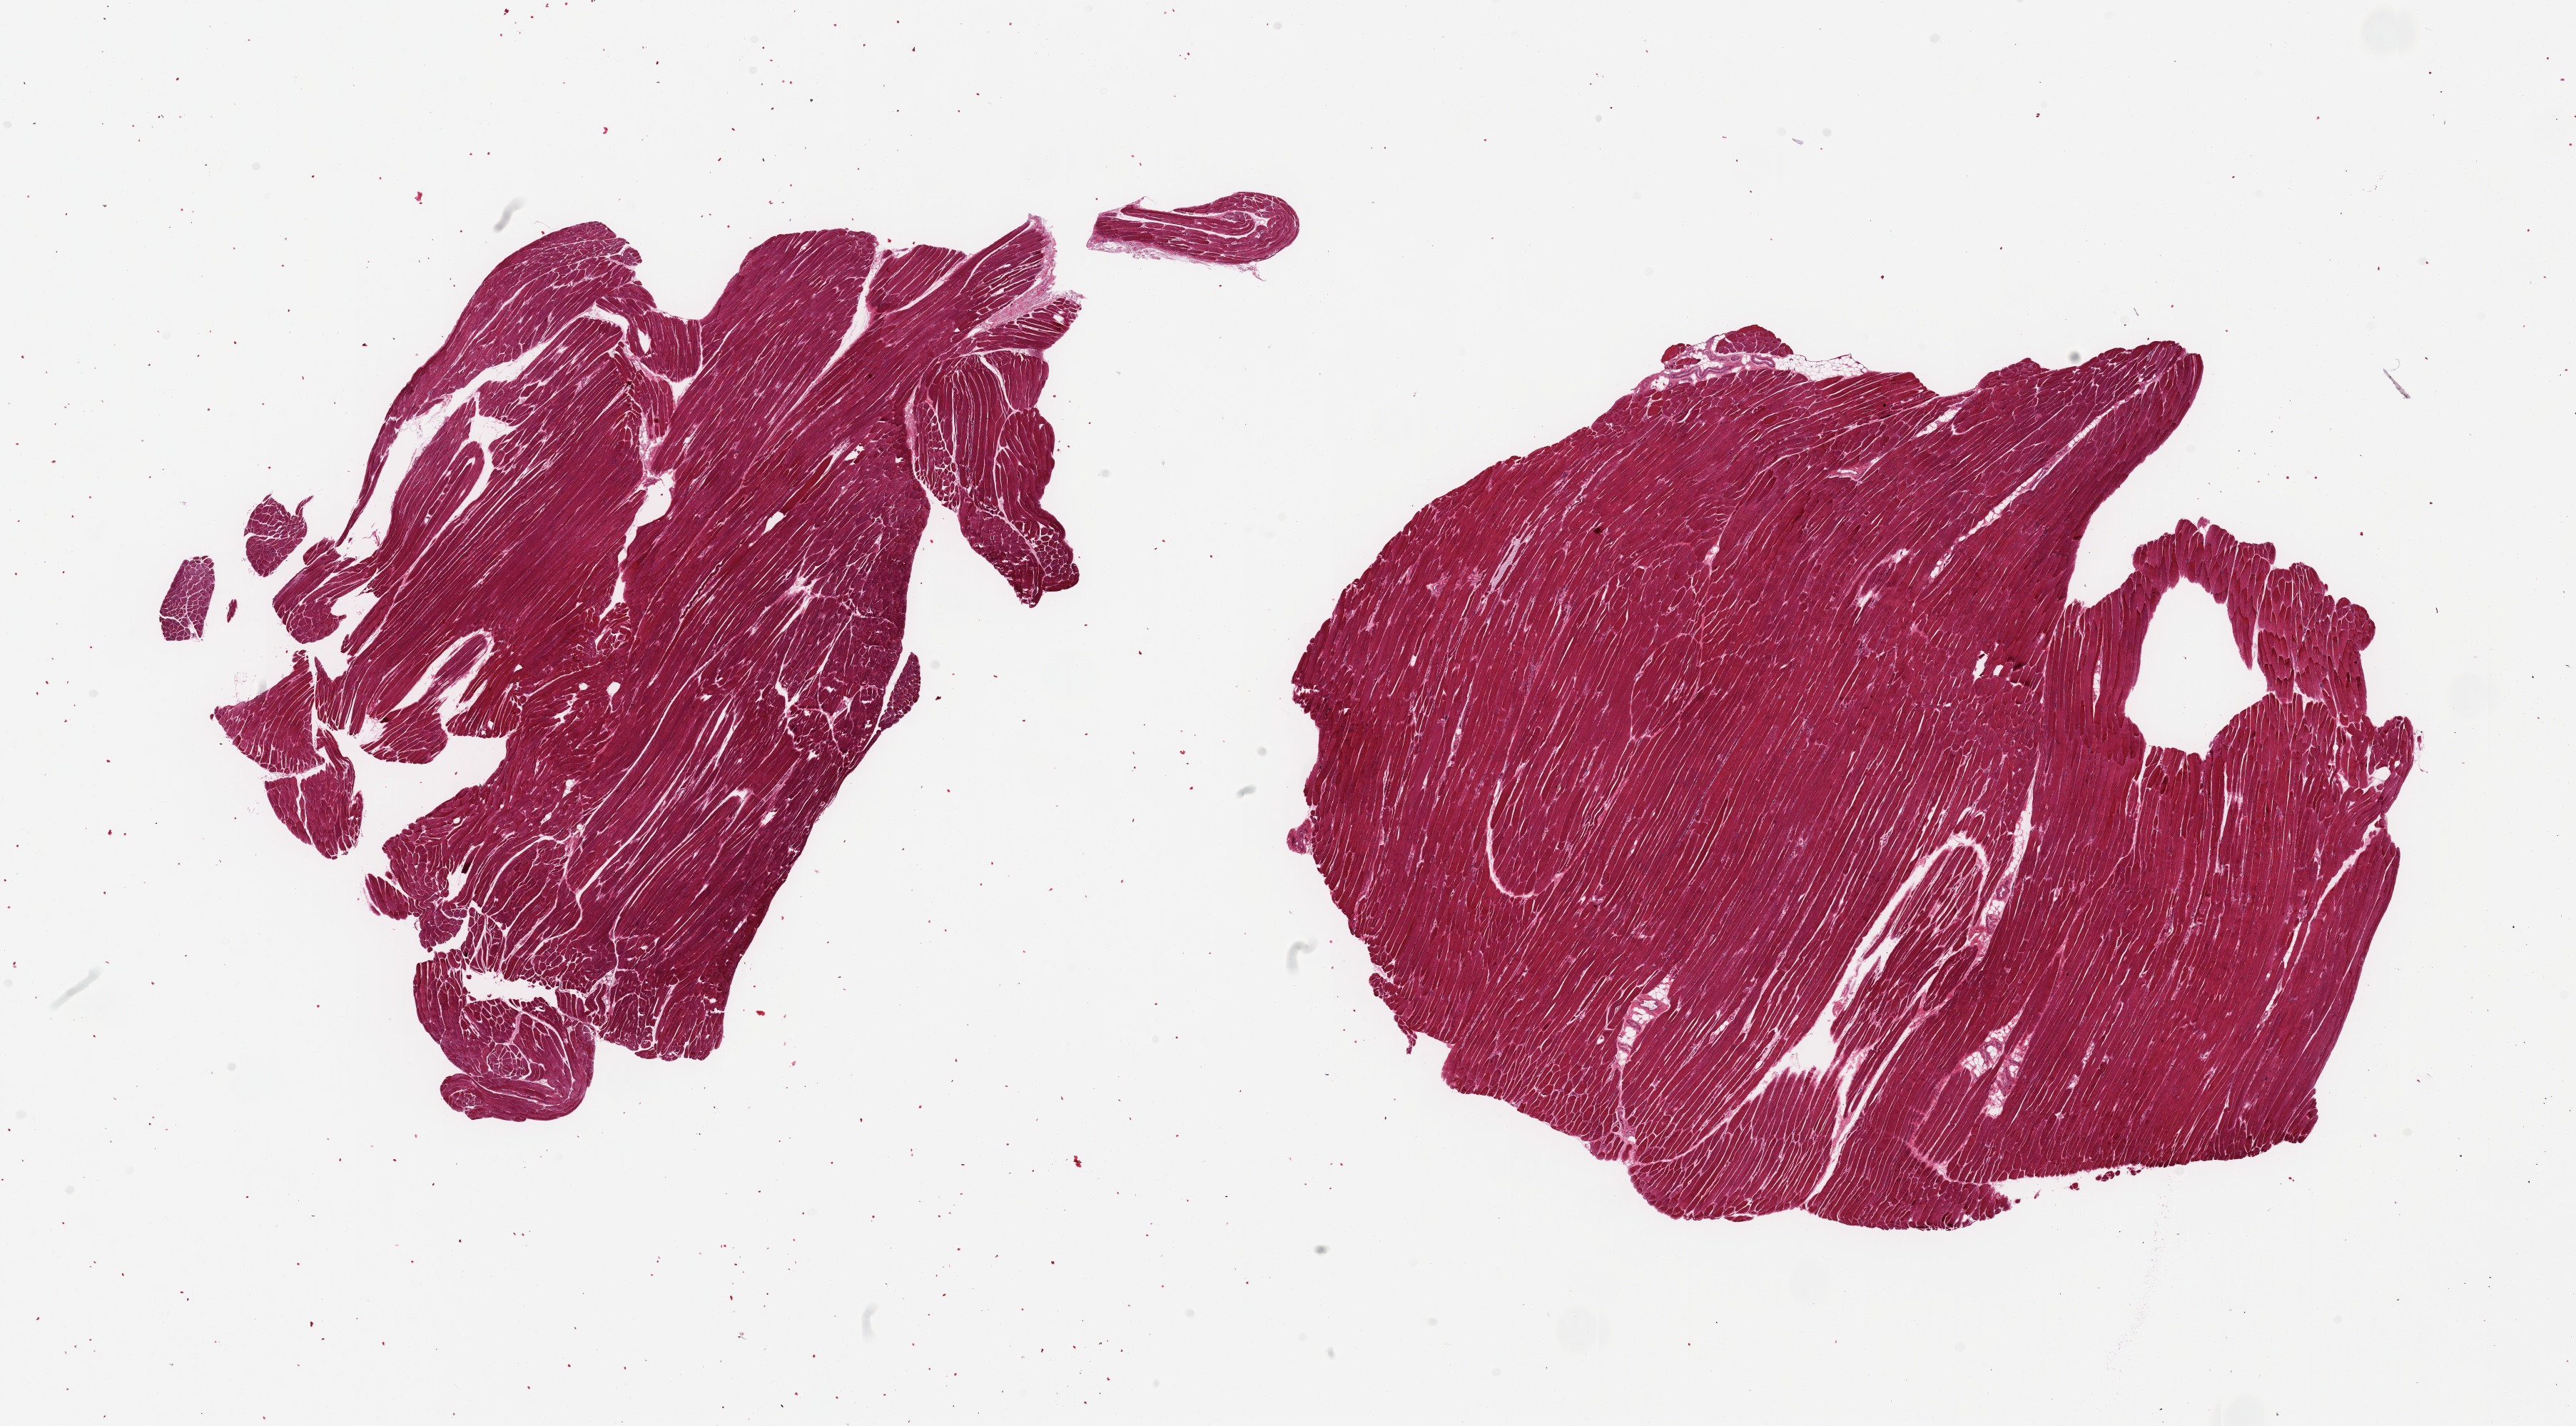
Digitized H&E-stained section, brightfield, whole scanned area (about 28.5 x 15.8 mm) shown as a low-resolution overview, PAXgene-fixed, paraffin-embedded tissue, section of skeletal muscle (target tissue), donor tissue sample. Donor sex: male.
Reviewer comment on this tissue sample: 2 pieces; skeletal muscle, trivila fat component.